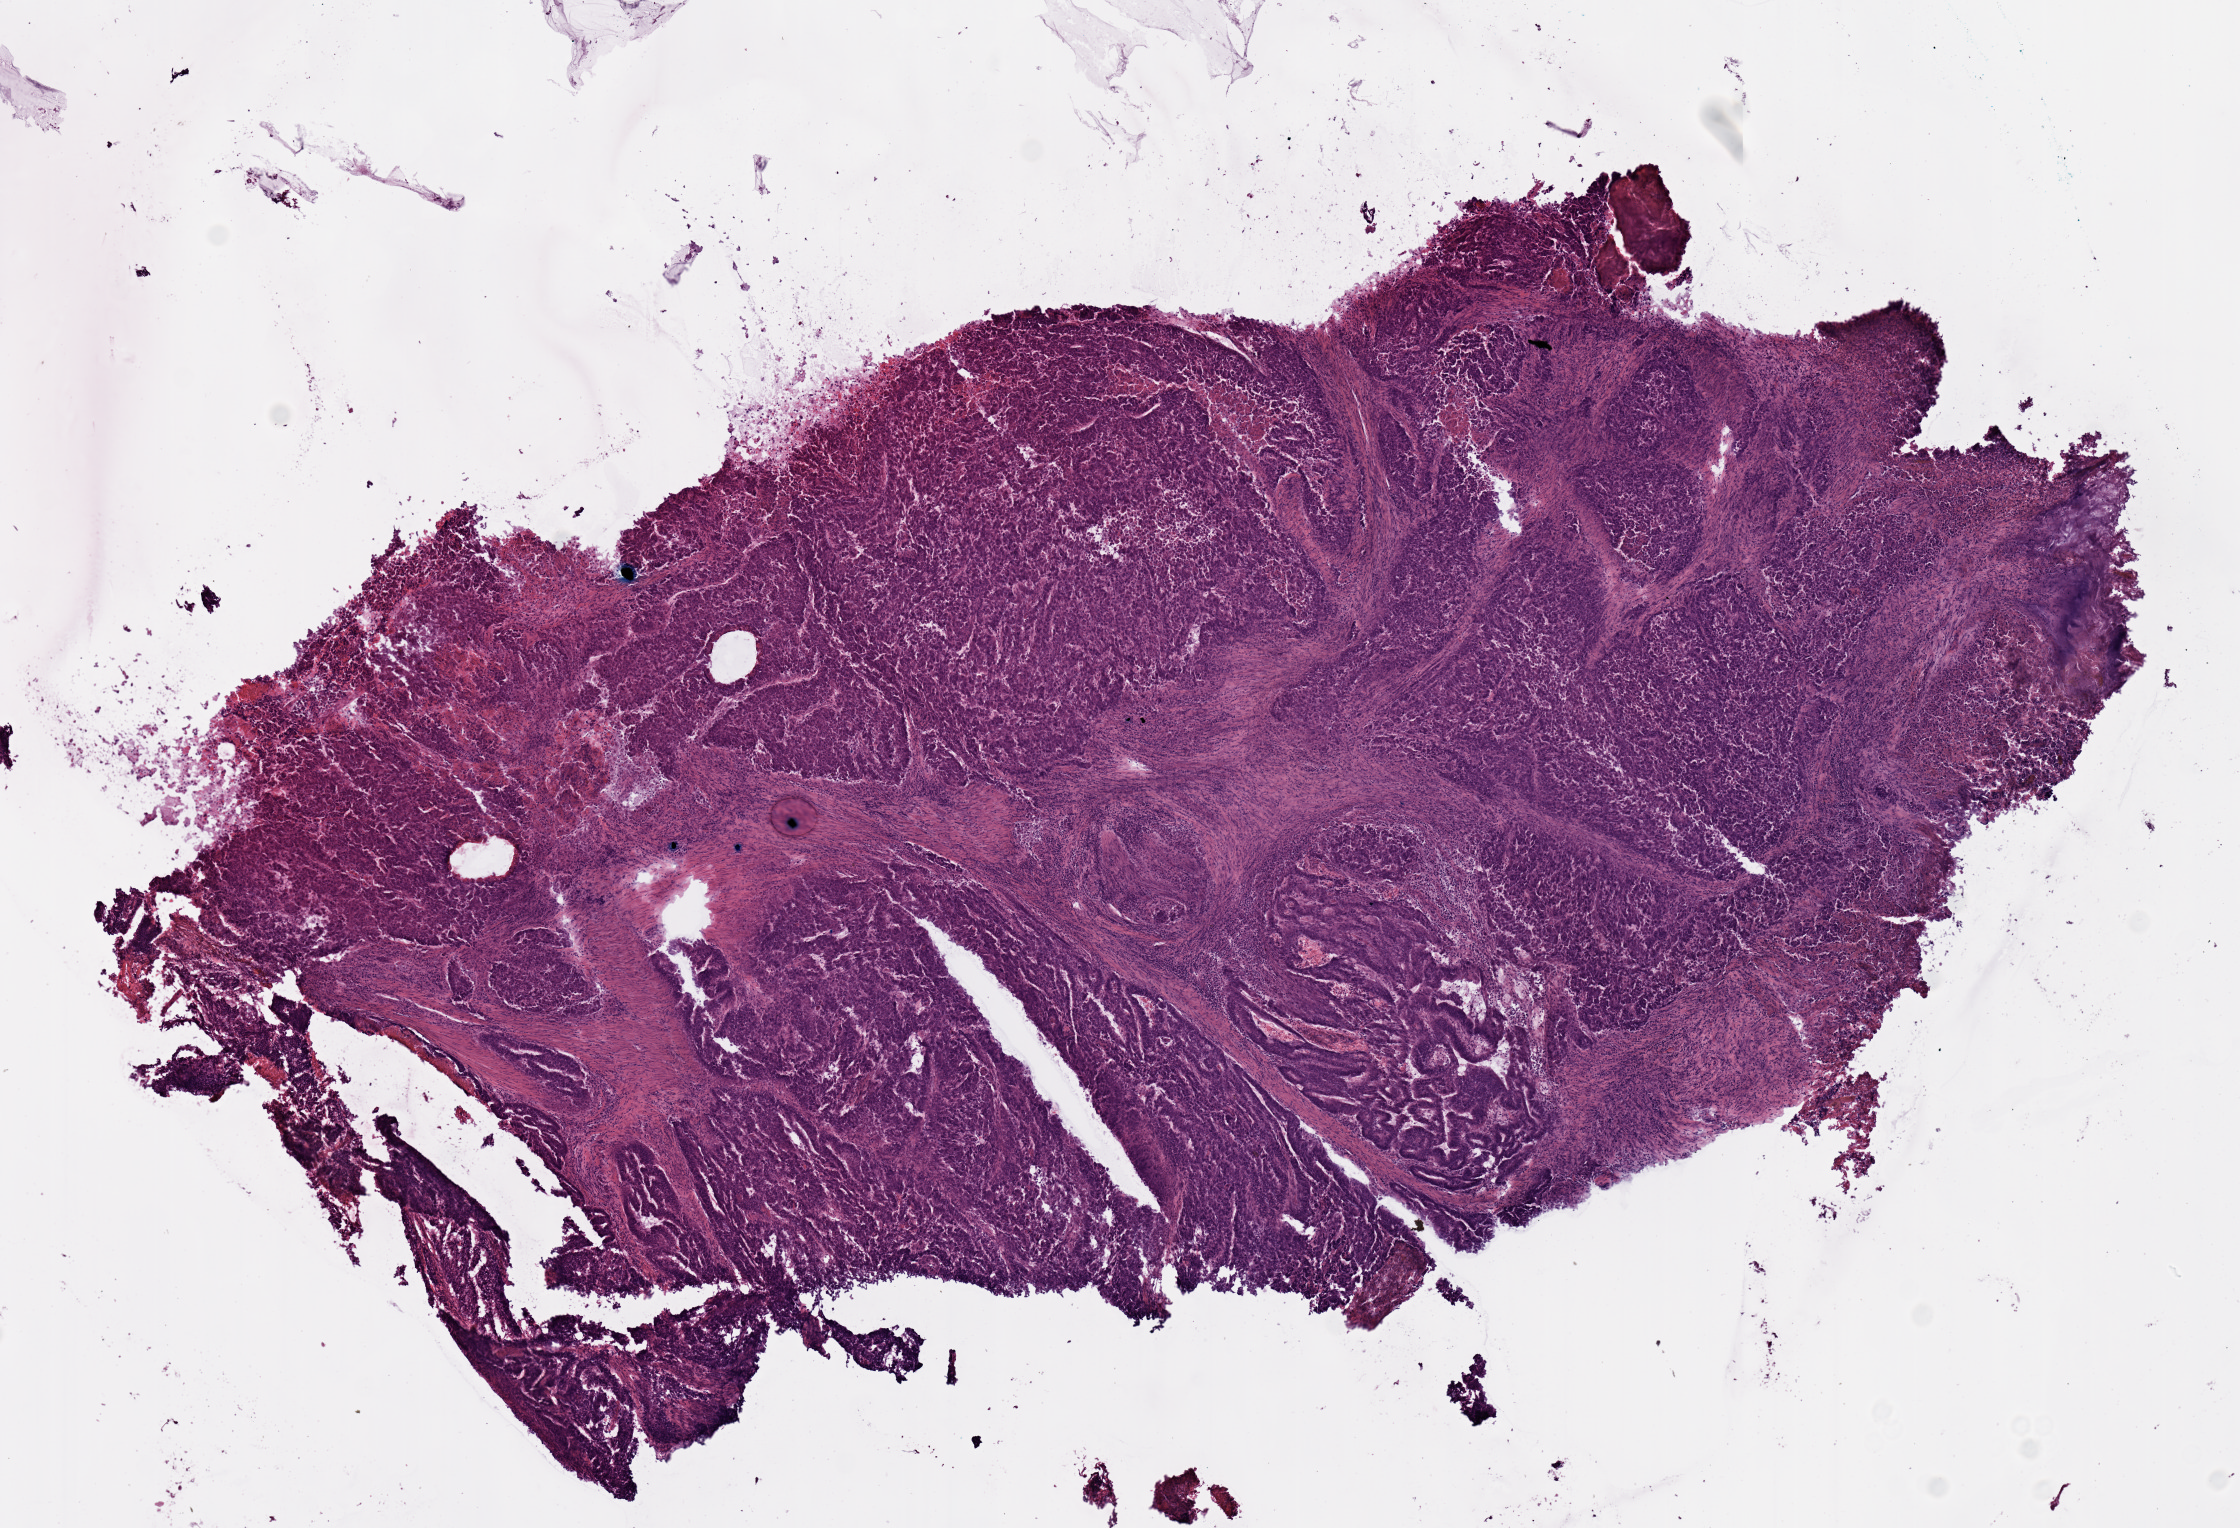
Whole-slide histology image, Hematoxylin and eosin (H&E) stained, whole scanned area (about 8.9 x 6.0 mm, slide scanned at 20x) shown as a low-resolution overview, frozen section, sample: primary tumour, rectum. Patient: male, age at initial diagnosis 57 years. Slide review estimates, as recorded: tumour cells 90%, tumour nuclei 75%, normal cells 0%, stromal cells 5%, necrosis 5%.
Lymph nodes positive (case pathology): 0 of 18 examined. AJCC pathologic stage: IIA (7th edition). Histologic diagnosis: Adenocarcinoma, NOS.